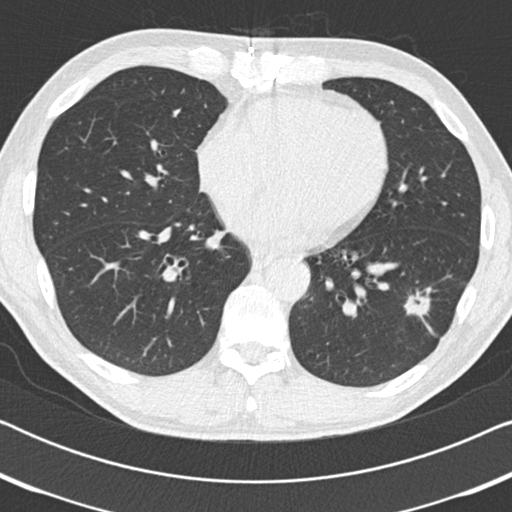
Low-dose screening chest CT, one axial slice; slice 76 of 186 in the series (ordered by position); 120 kVp; lung window (W 1500 / L -600 HU); 2 mm slice thickness; 512 × 512 image matrix, field of view 330 × 330 mm.
Annotated regions visible in this slice (outlined manually by an expert reader):
- lesion 1 (tumor, lower lobe of left lung): bounding box [x1, y1, x2, y2] px = [404, 293, 430, 317]